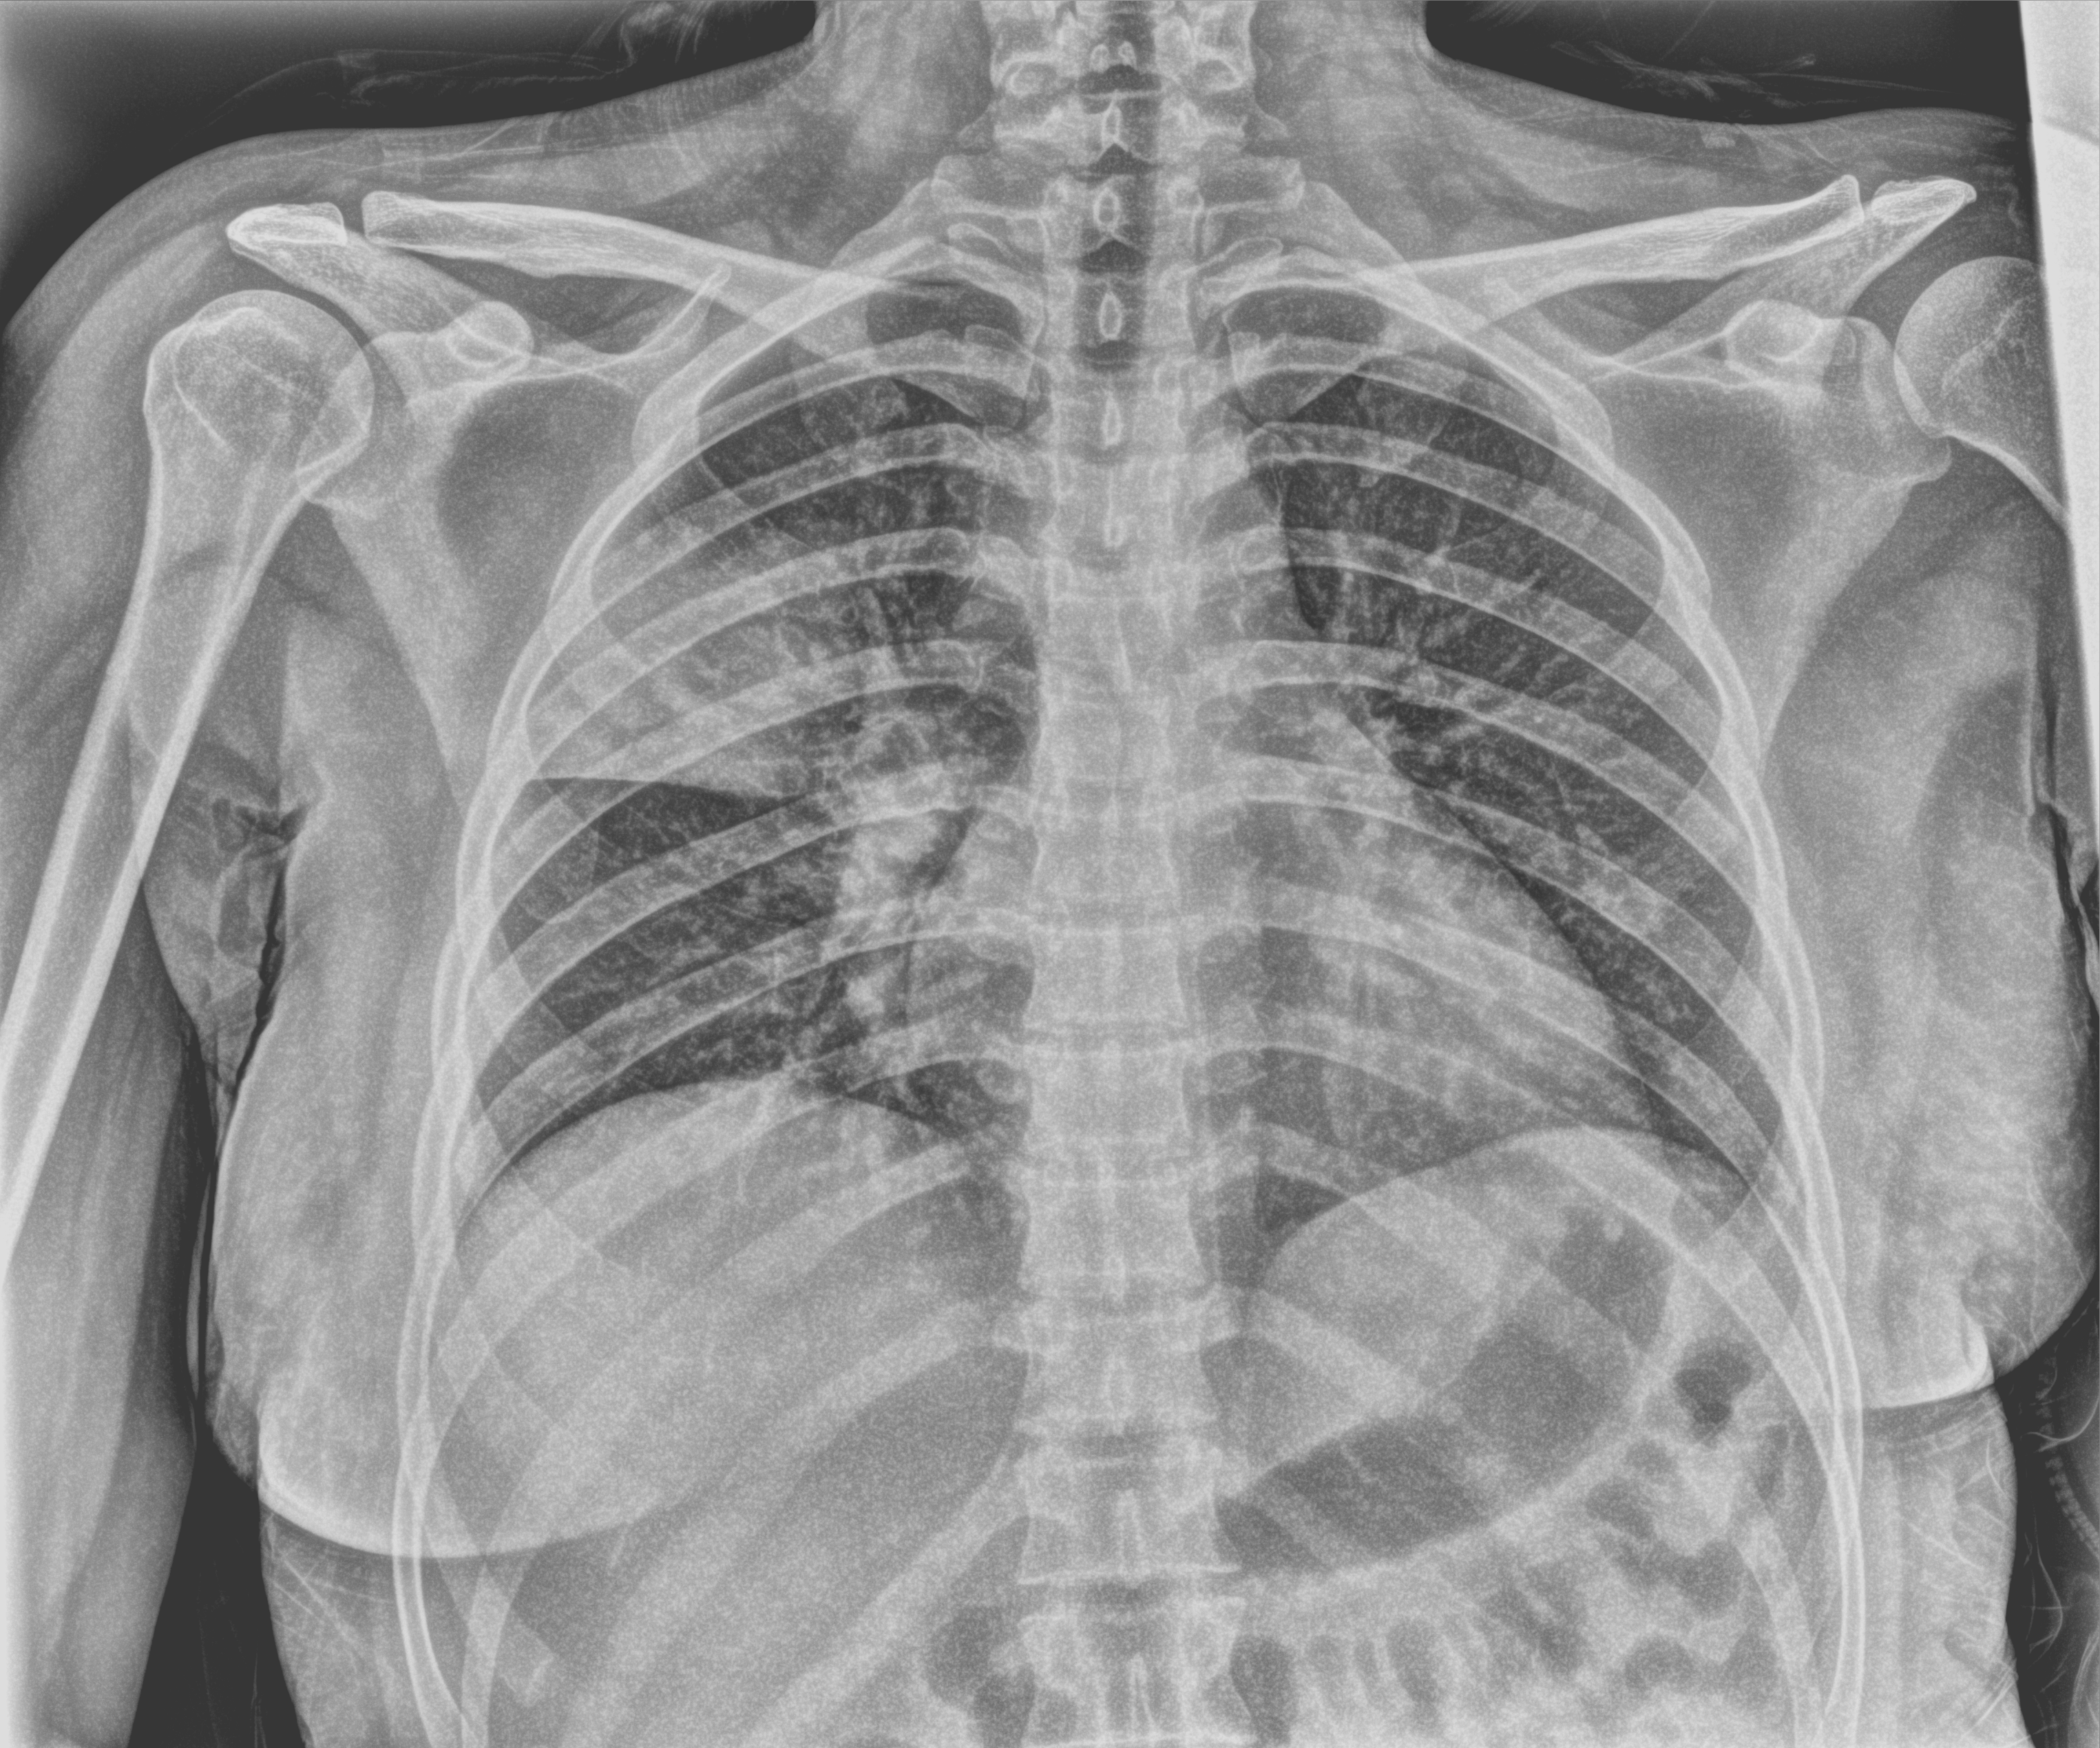
Bedside chest radiograph (computed radiography). Patient hospitalised with COVID-19; female, aged 18–59 years.
From the hospital-stay record, not from the radiograph (when in the stay this image was taken is not recorded): admitted to intensive care during this hospital stay: no.